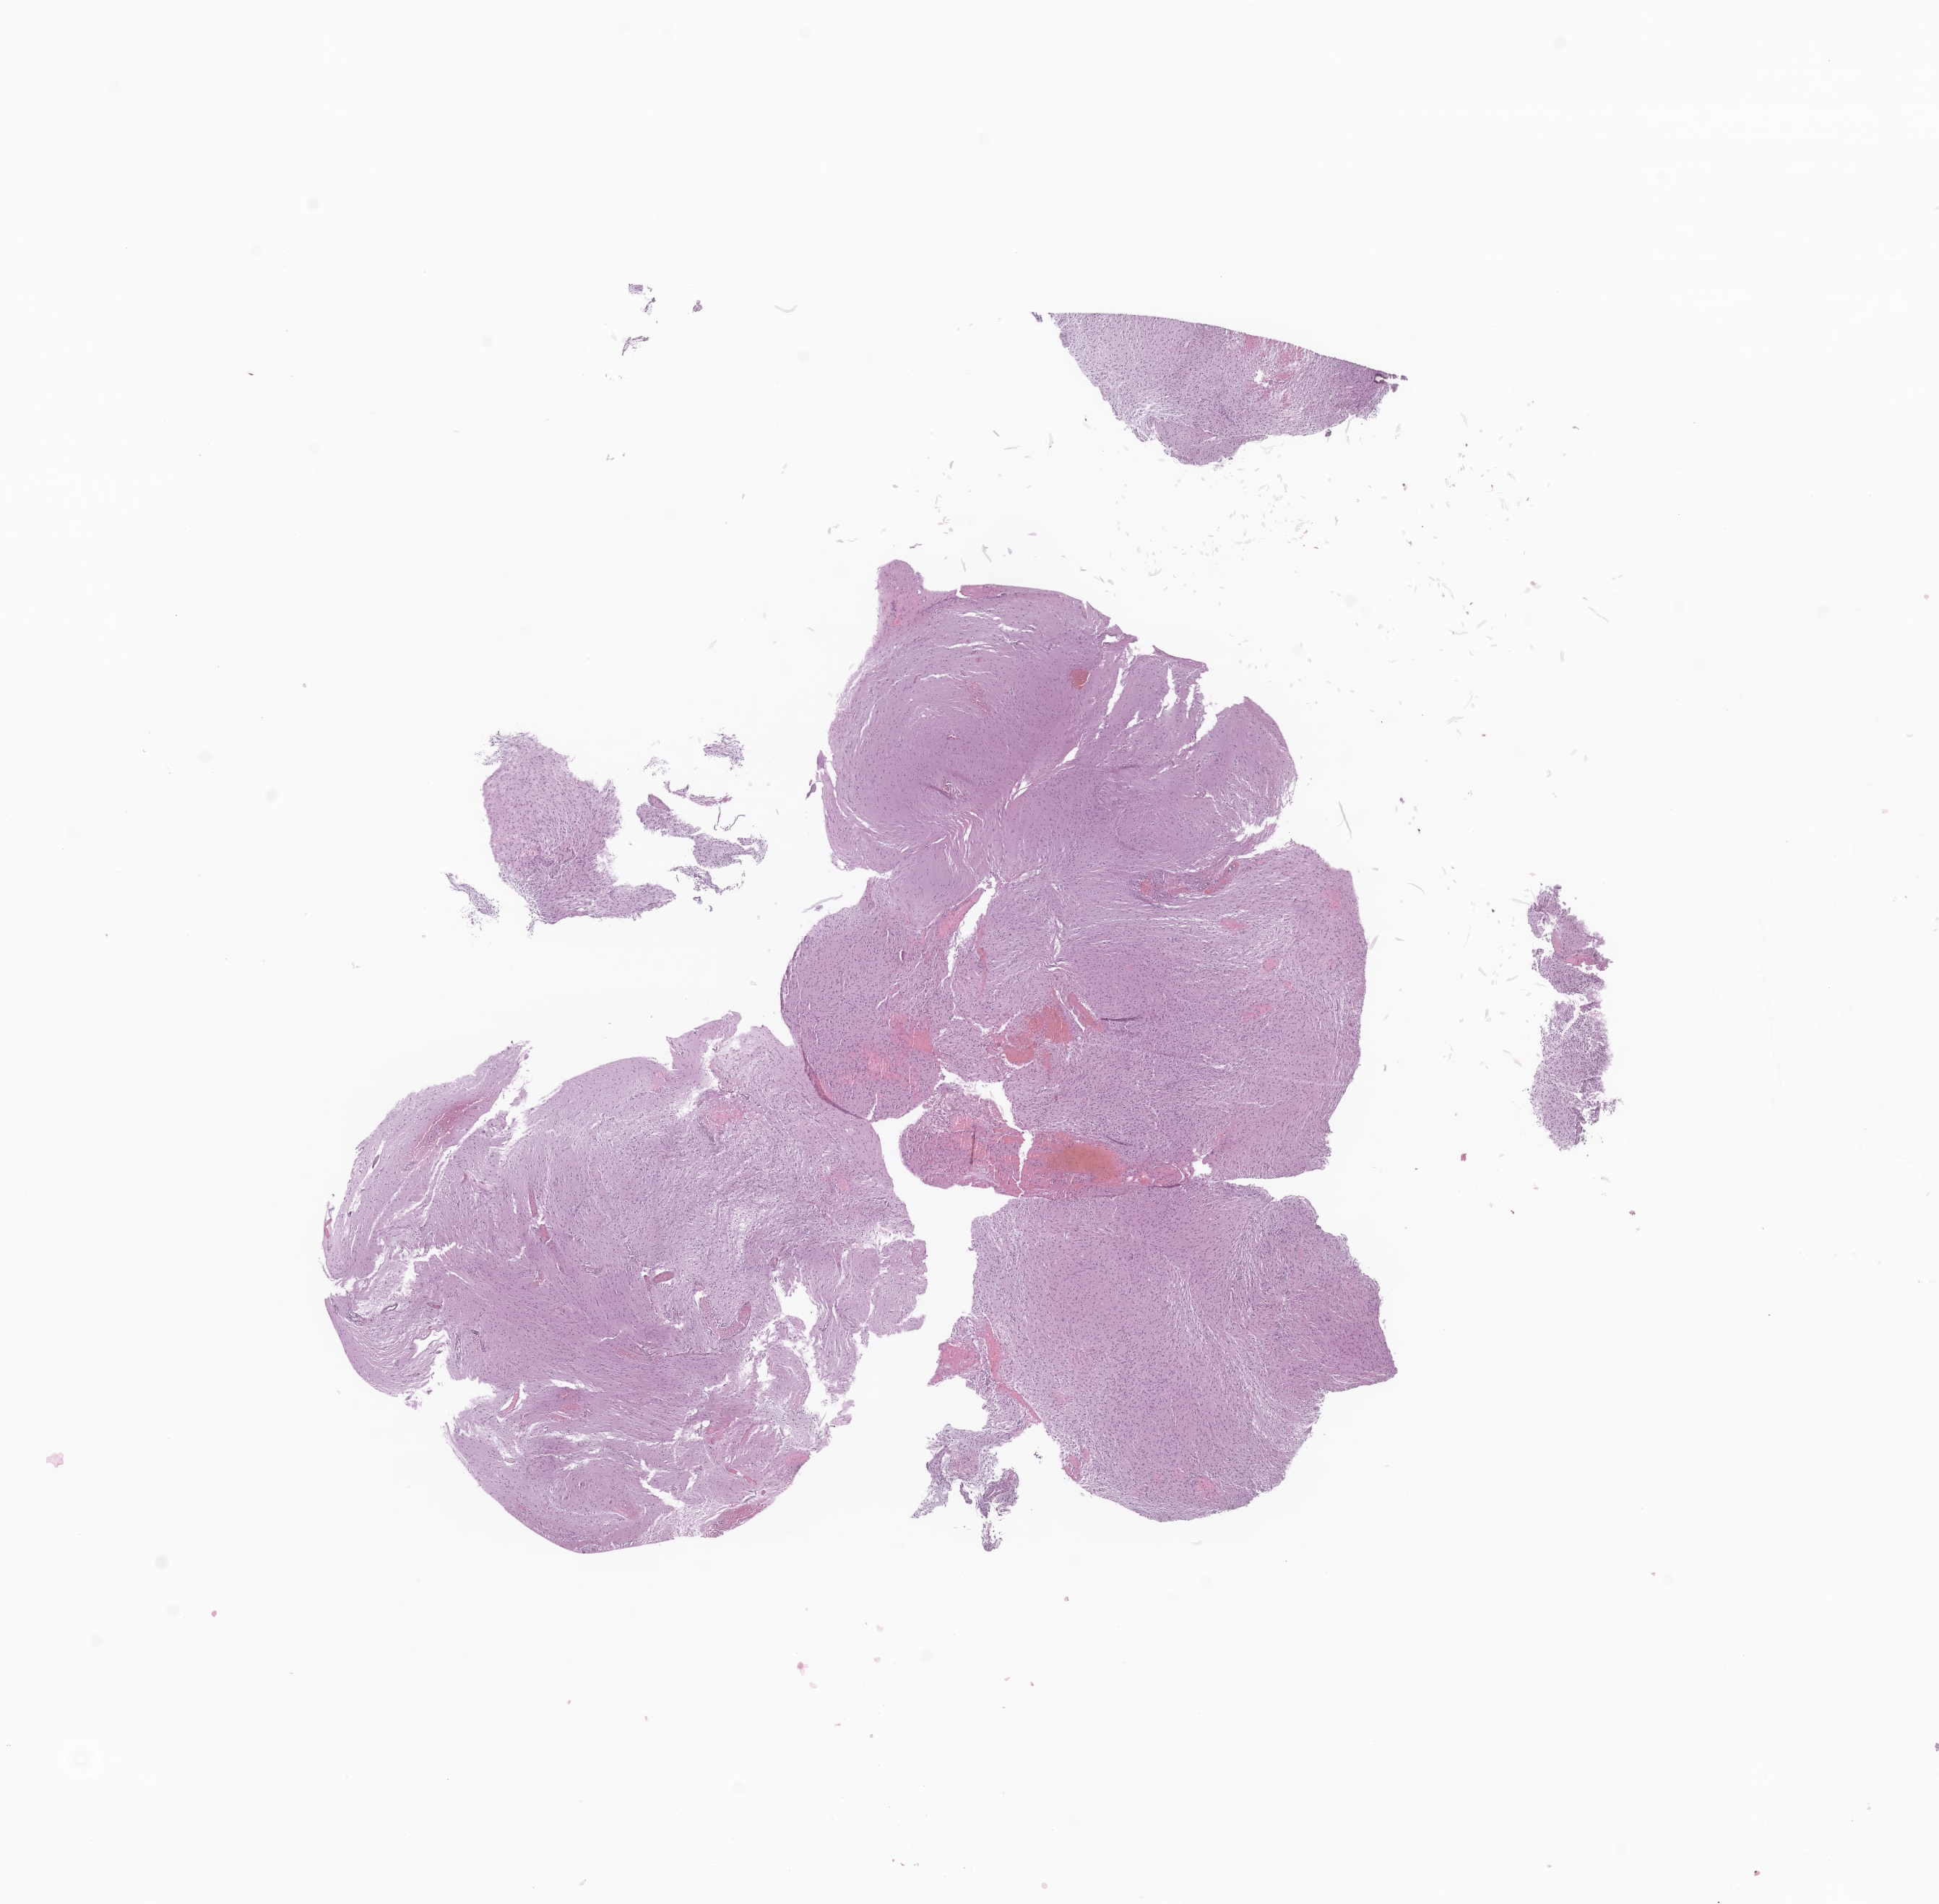
Digitized H&E-stained section of tumor tissue from the brain, a low-resolution overview of the entire scanned area, about 11.3 x 11.1 mm; formalin-fixed paraffin-embedded section. Female patient, age 211 months (17 years 7 months).
Diagnosis (ICD-O-3 morphology term): Pilocytic astrocytoma.